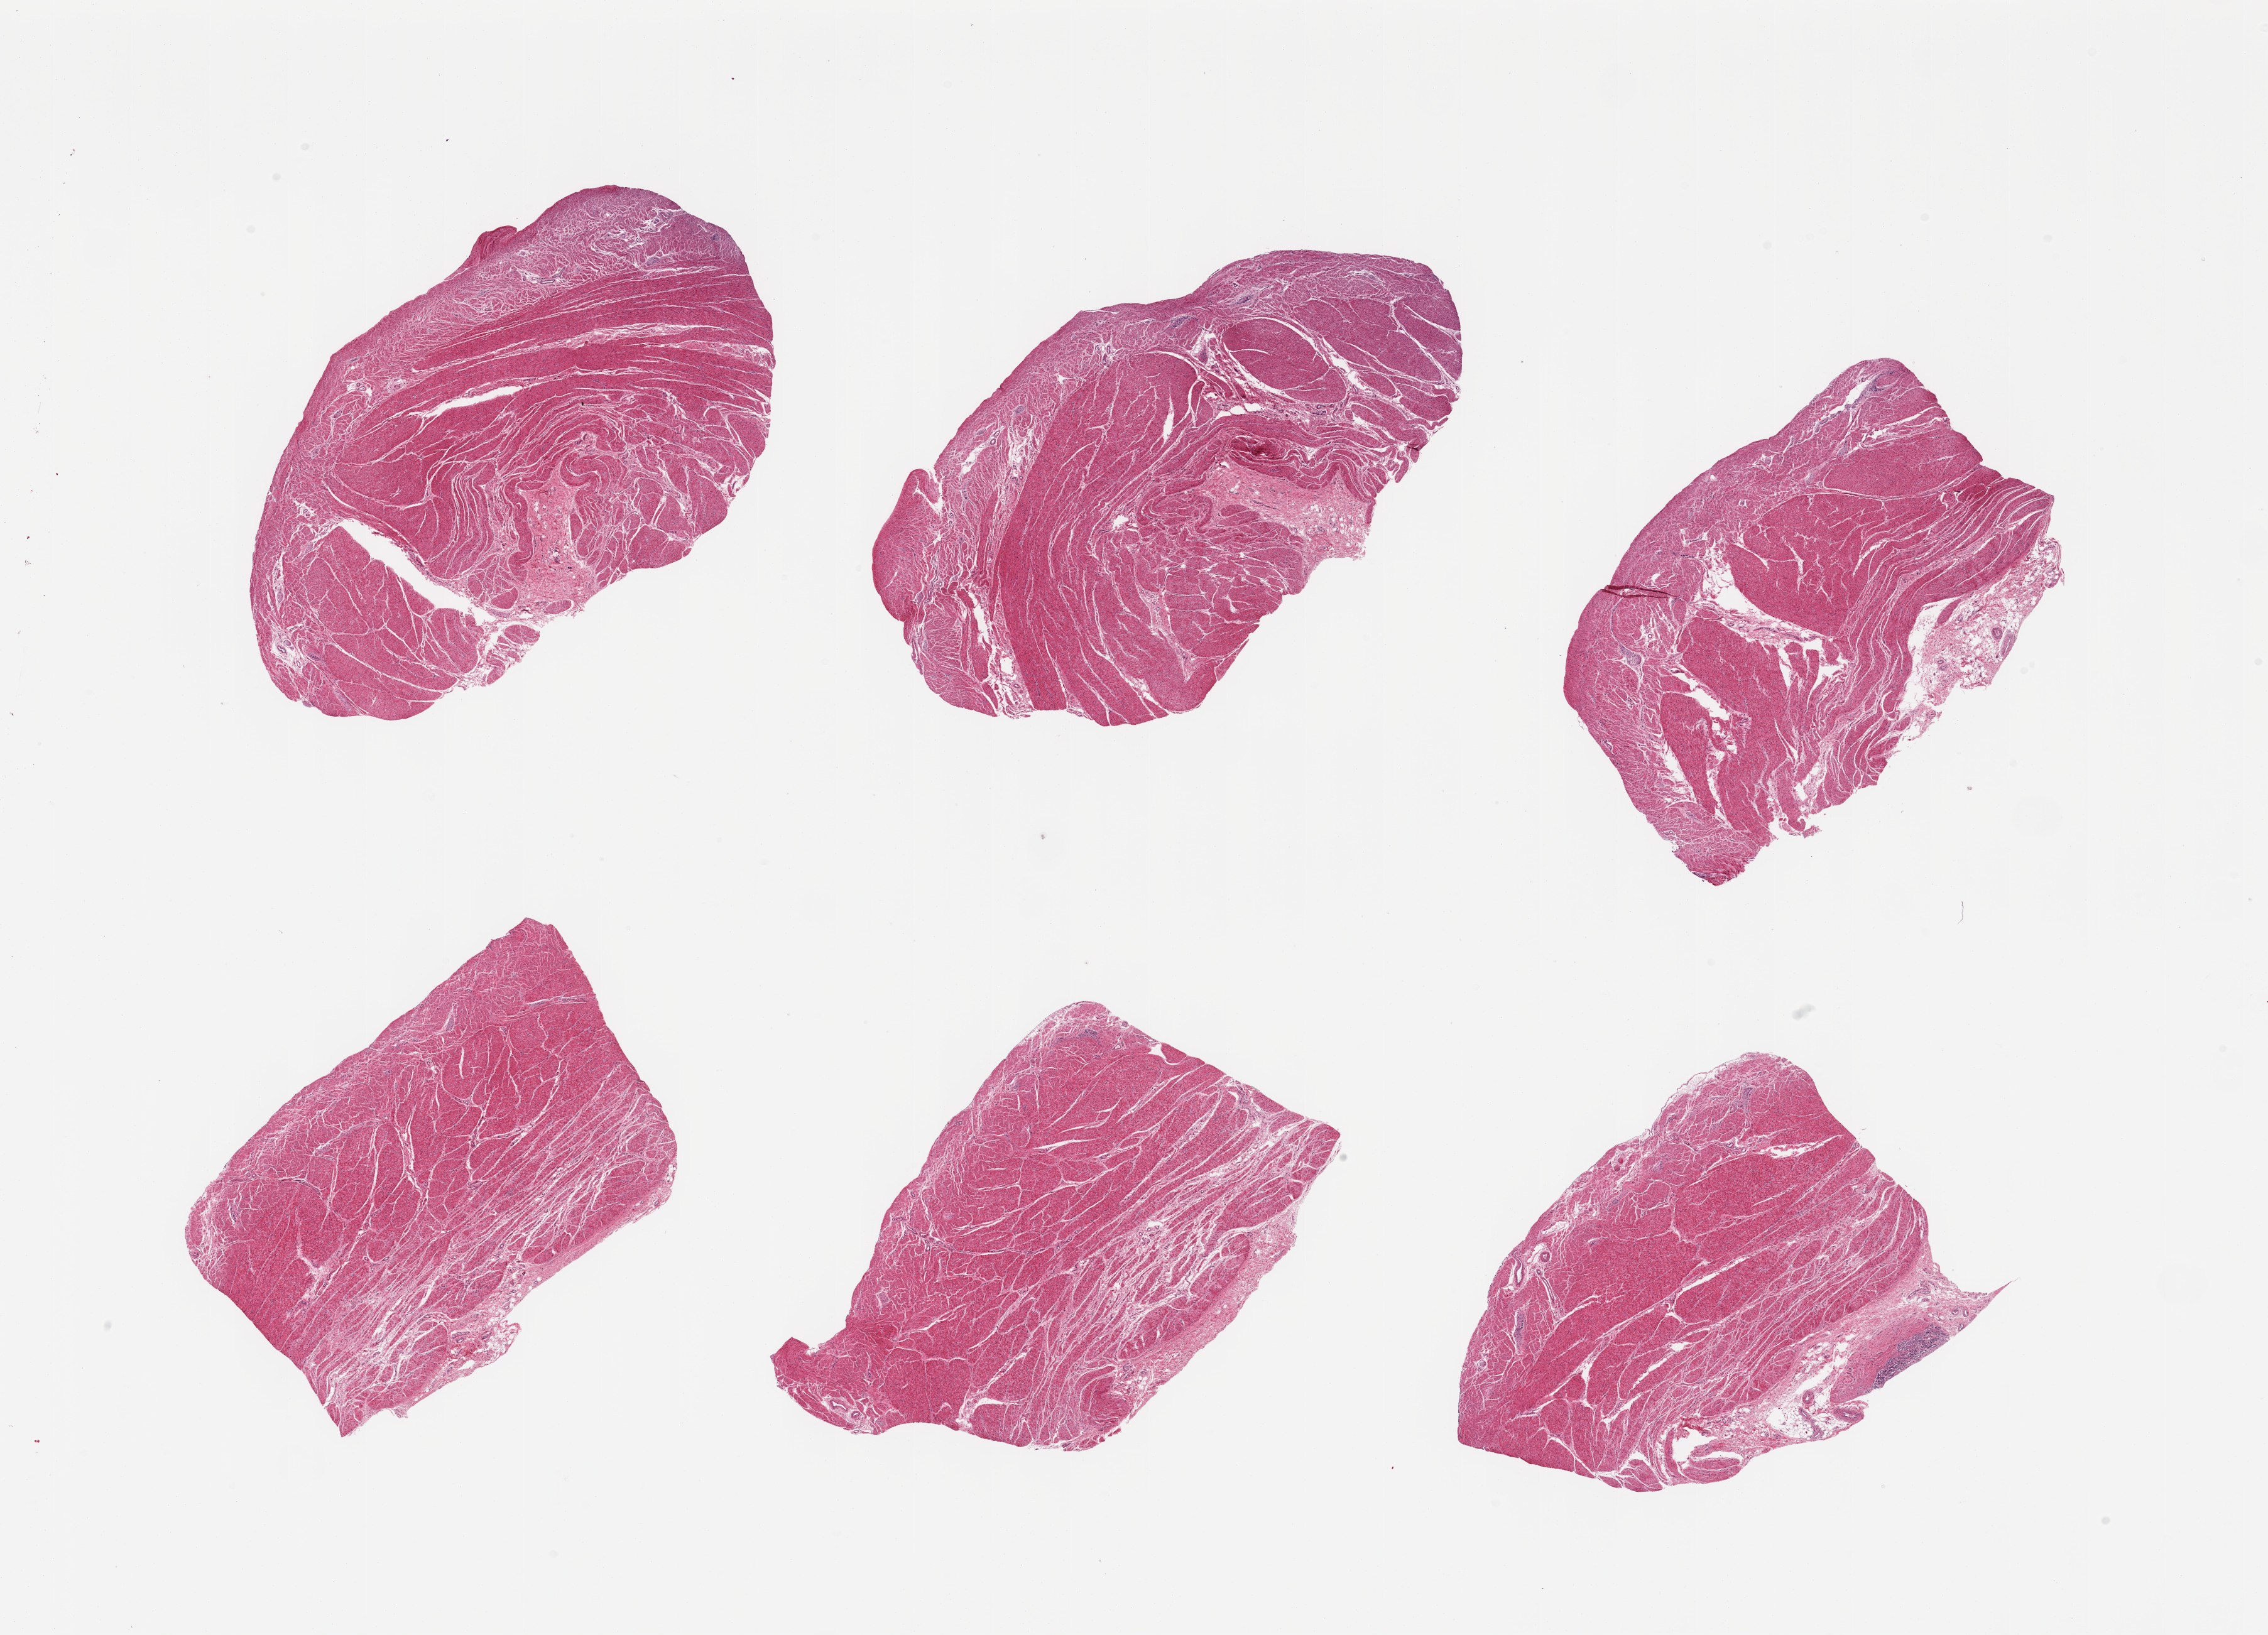
Whole-slide image, haematoxylin and eosin stain, brightfield, shown as a low-resolution overview of the whole scanned area (about 28.5 x 20.6 mm, acquisition: 20x scan). PAXgene-fixed, paraffin-embedded tissue. Sampled site (target tissue): gastroesophageal junction. Tissue donor sample. Donor sex: male.
* pathologist's review note for this sample: 6 pieces; small [10%] mucosal remnant on 1 piece